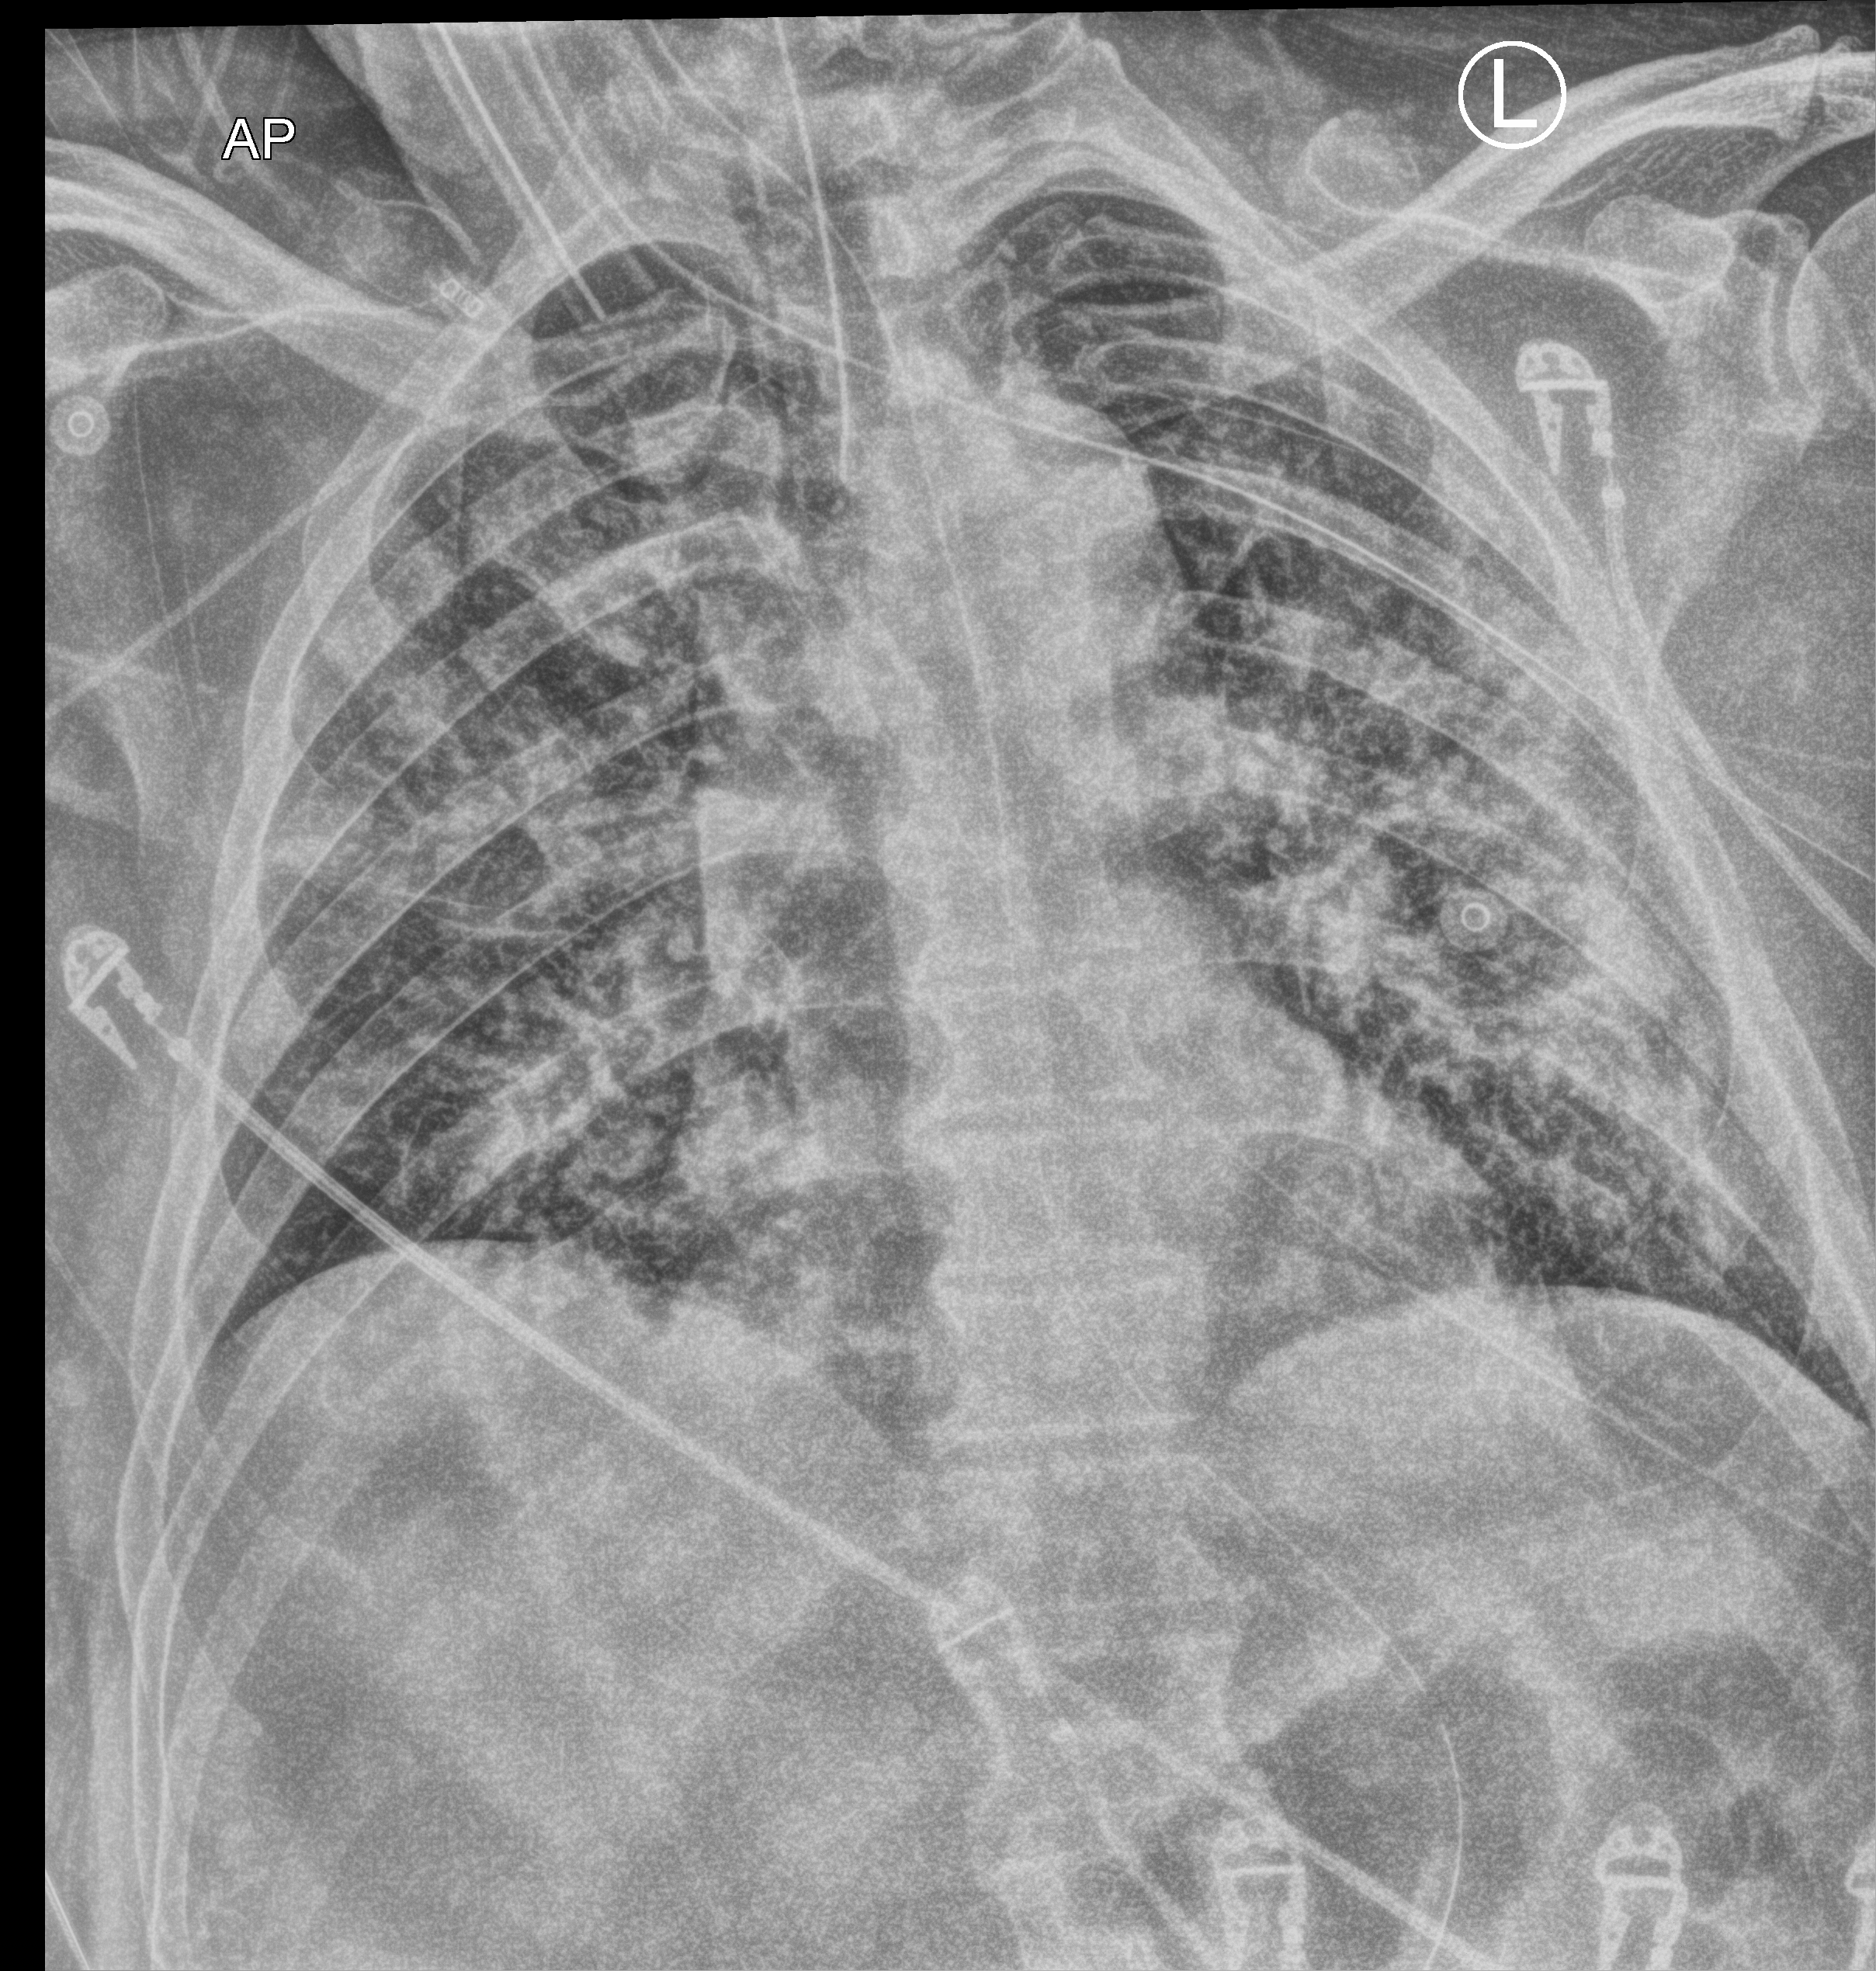
Portable chest radiograph. Patient hospitalised with COVID-19; male, aged 60–74 years.
Admission-level facts for this patient (not findings on this image; timing relative to this image not recorded): mechanically ventilated during this hospital stay: yes.